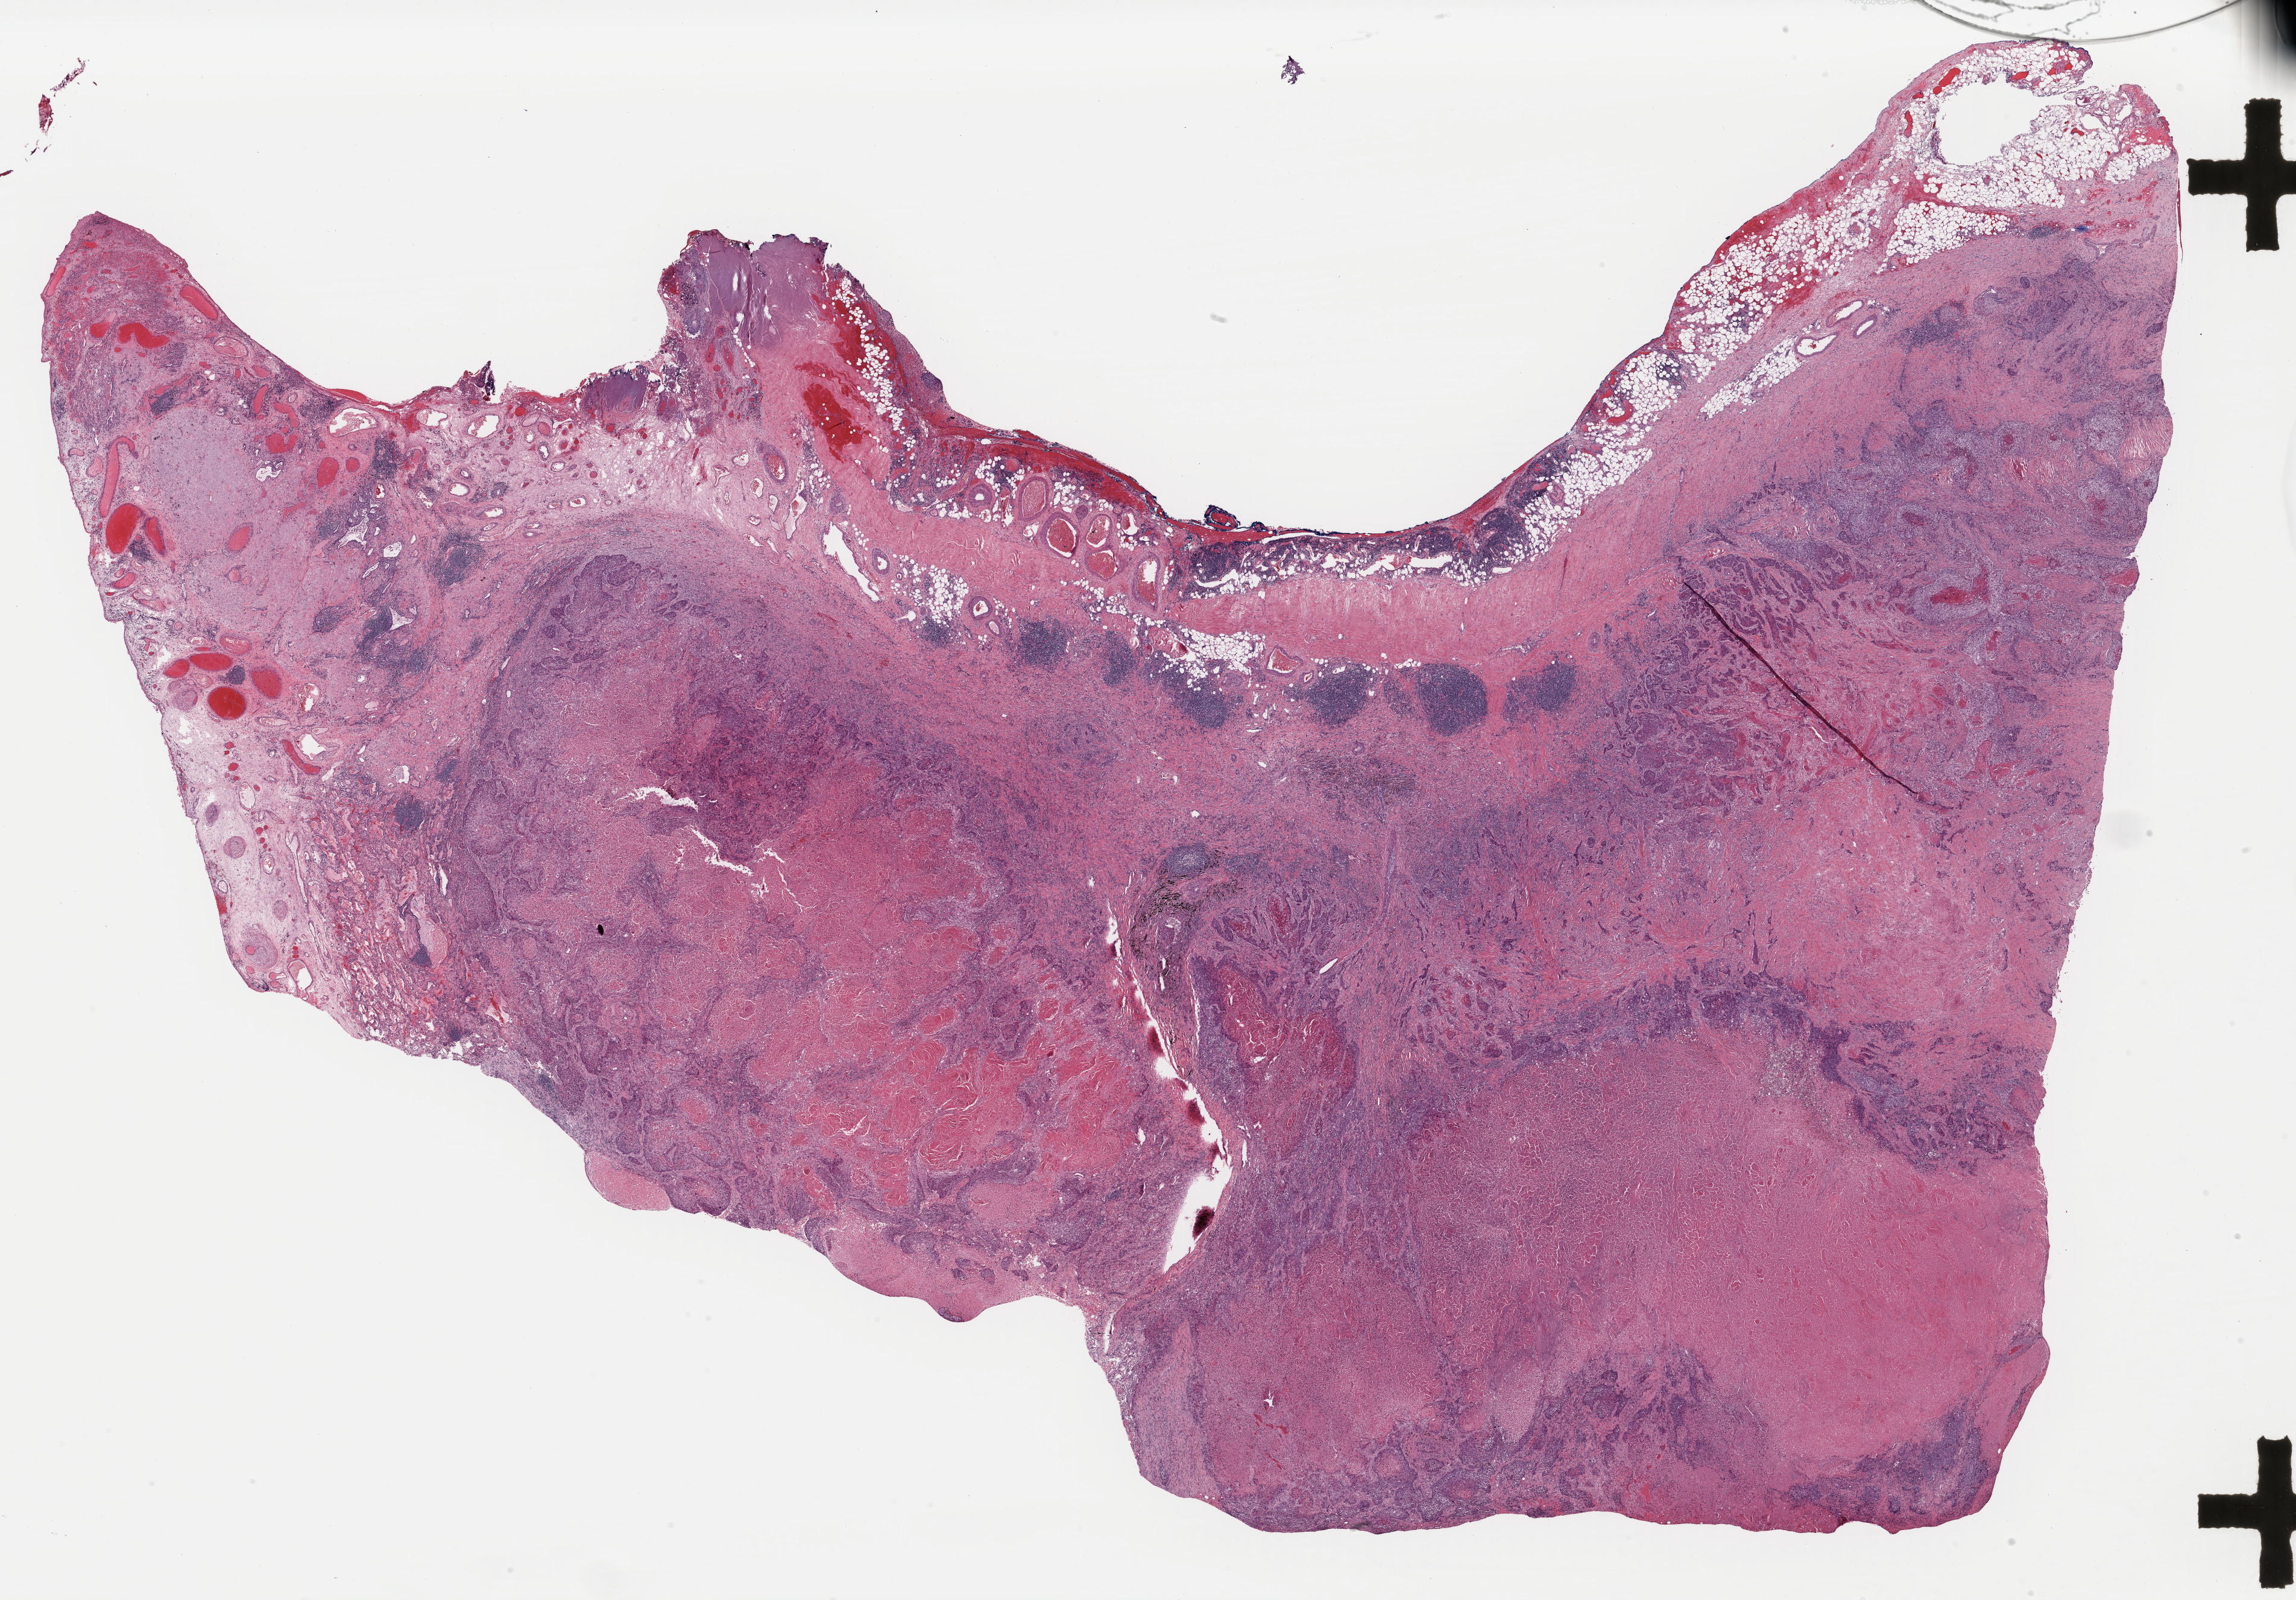
Whole-slide histology image, H&E-stained — a low-resolution overview of the entire scanned area, about 30.0 x 20.9 mm. FFPE section. Sample: primary tumour, lung. Male, age 80 years at initial diagnosis.
Pathologic diagnosis: Squamous cell carcinoma, NOS. AJCC pathologic stage: IIB. Laterality: right.